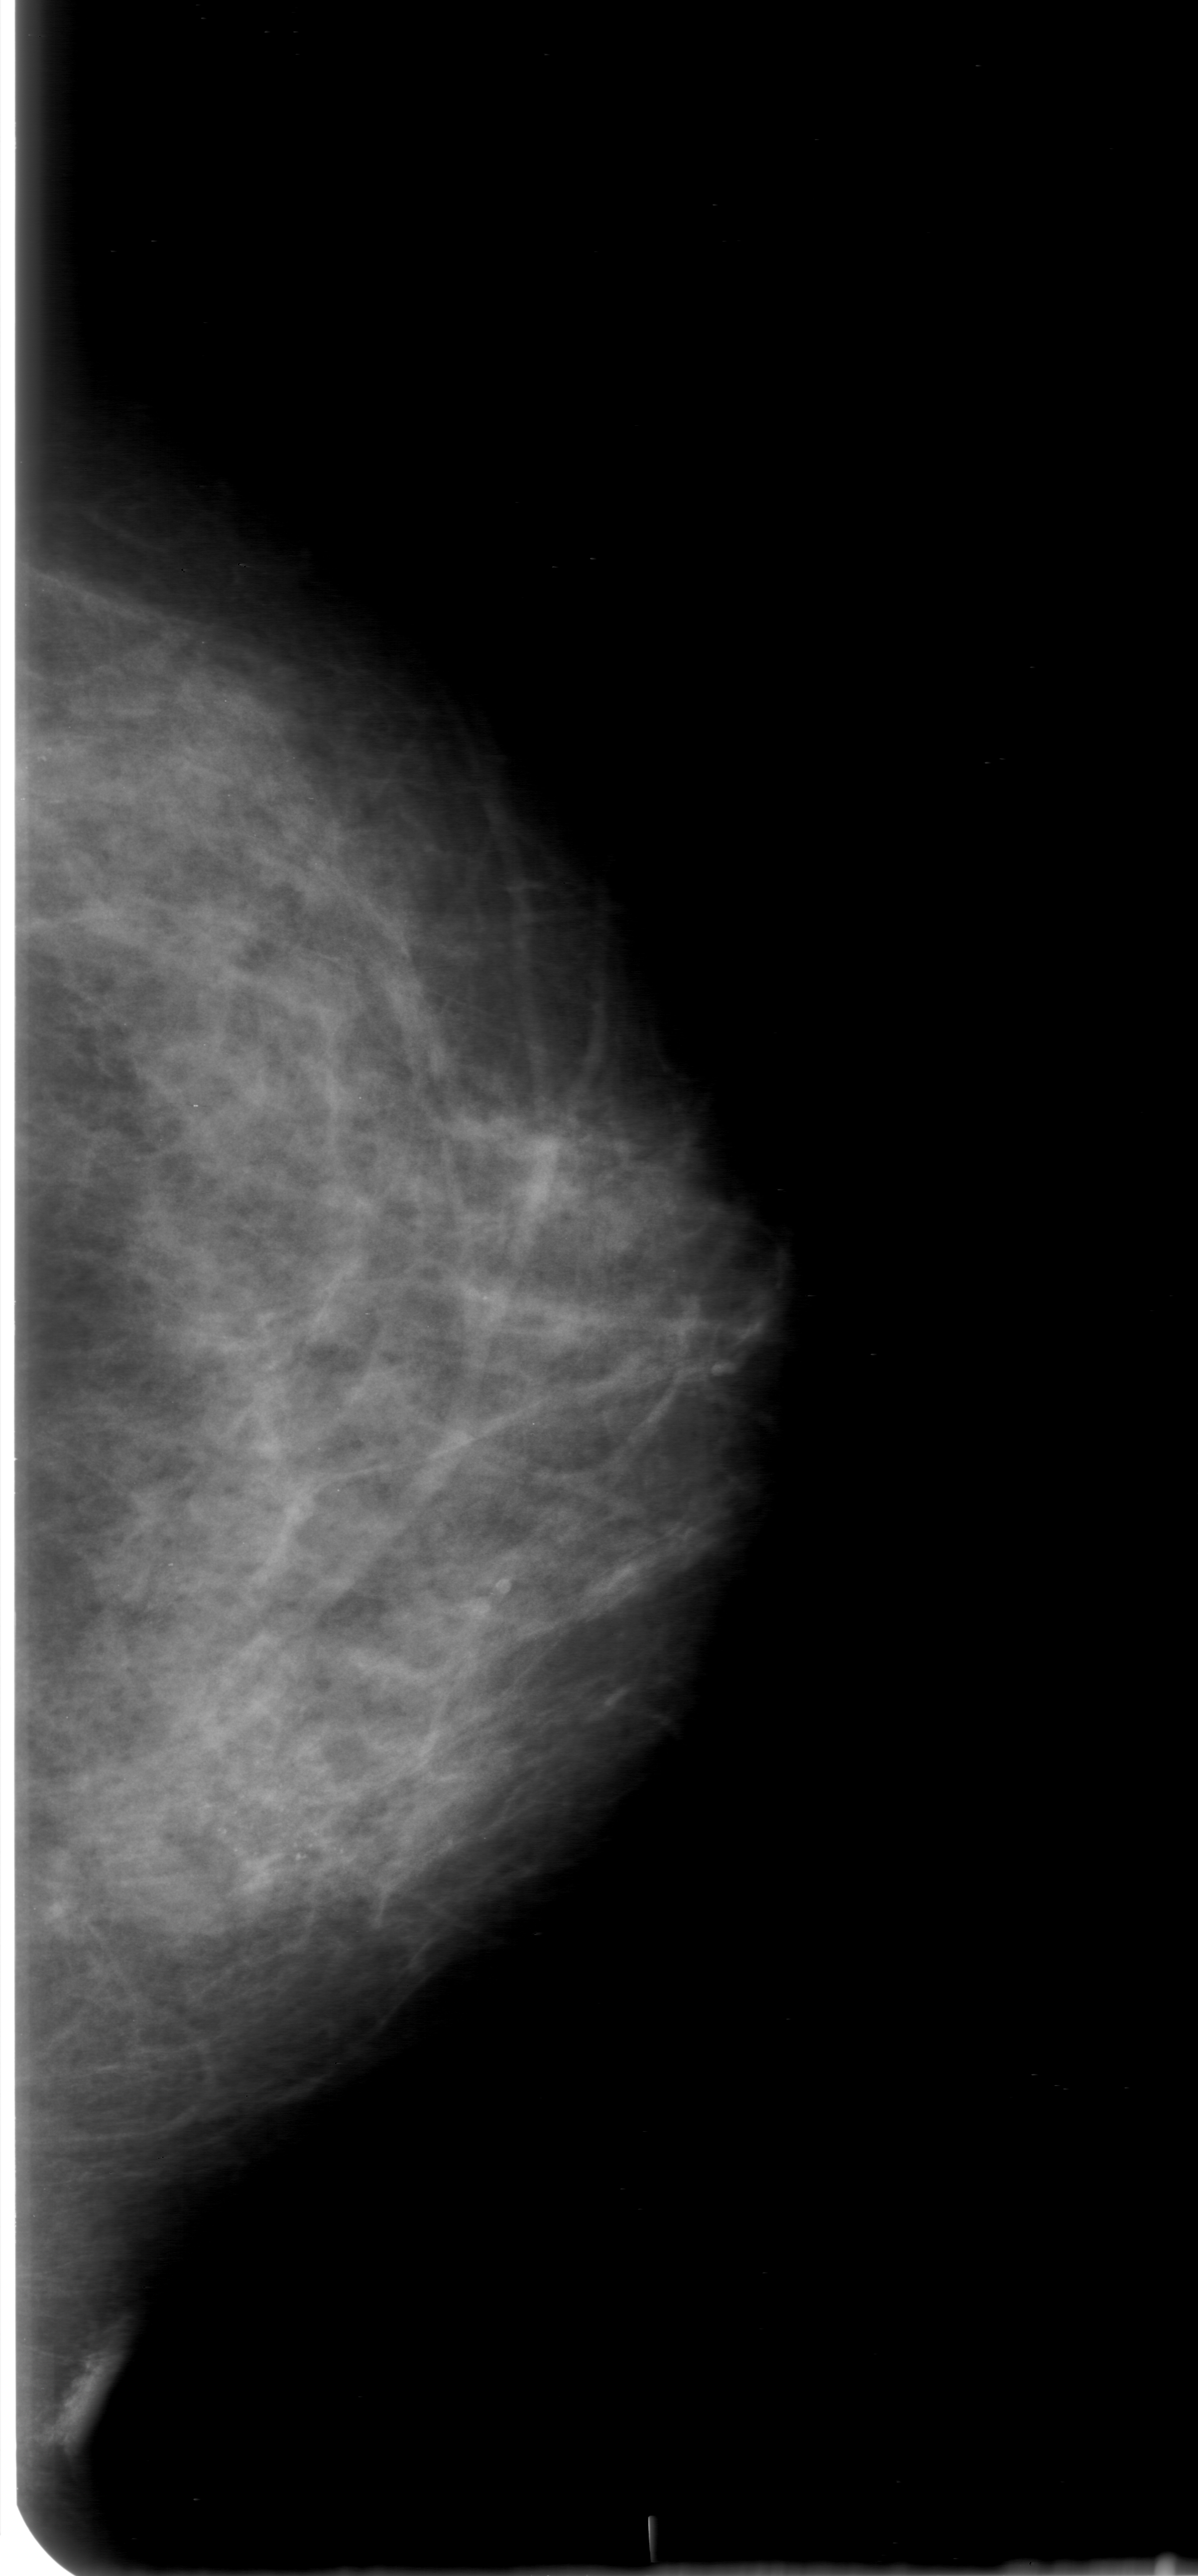
Digitized screen-film mammogram; left breast; CC view; breast composition: heterogeneously dense (BI-RADS density category 3 of 4); 1198 × 2576 image matrix.
Marked abnormalities (boxes around the expert regions of interest):
- calcifications, morphology pleomorphic, distribution clustered; BI-RADS assessment category 0 (incomplete: needs additional imaging); pathology (as recorded): malignant: bounding box <147,1656,466,1971> (left, top, right, bottom; pixels)